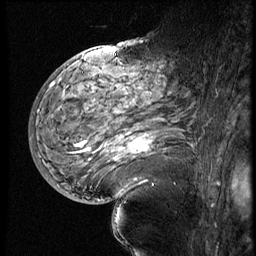
Breast MRI (dynamic contrast-enhanced), one sagittal slice; position 34 of 60 along the scan axis; 4 images stored at this slice position (order not interpretable as contrast timing); 1.5 T; TE 4.2 ms, TR 9 ms; 256 × 256 image matrix, field of view 180 × 180 mm. Patient: female, 56 years. Case-level facts recorded for this patient, not image findings: setting: breast cancer imaged before/during neoadjuvant chemotherapy; receptor status: HER2-positive.
Outlined on this slice (semi-automatically segmented with operator editing):
- analysis volume of interest (the breast-tissue region the enhancement analysis was run in; not a lesion): bounding box <82,83,199,177> (left, top, right, bottom; pixels)
- tumour enhancement mask (voxels above the 140 % enhancement threshold inside the analysis volume of interest): <116,133,152,161>